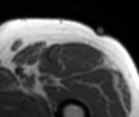
MRI of an extremity soft-tissue mass, one axial slice. Position 75 of 86 along the scan axis. MR volume resampled by the dataset authors to the PET/CT grid (not the native acquisition matrix). 3.27 mm slice thickness. 139 × 117 image matrix. Male patient. From the clinical record (not read from this slice): histological type: extraskeletal osteosarcoma; grade: high; site of the primary tumour: thigh.
Outlined on this slice (expert contour drawn on MRI and transferred to this co-registered scan by the dataset authors):
- gross tumour volume (mass): box from (x=52, y=41) to (x=103, y=67) px